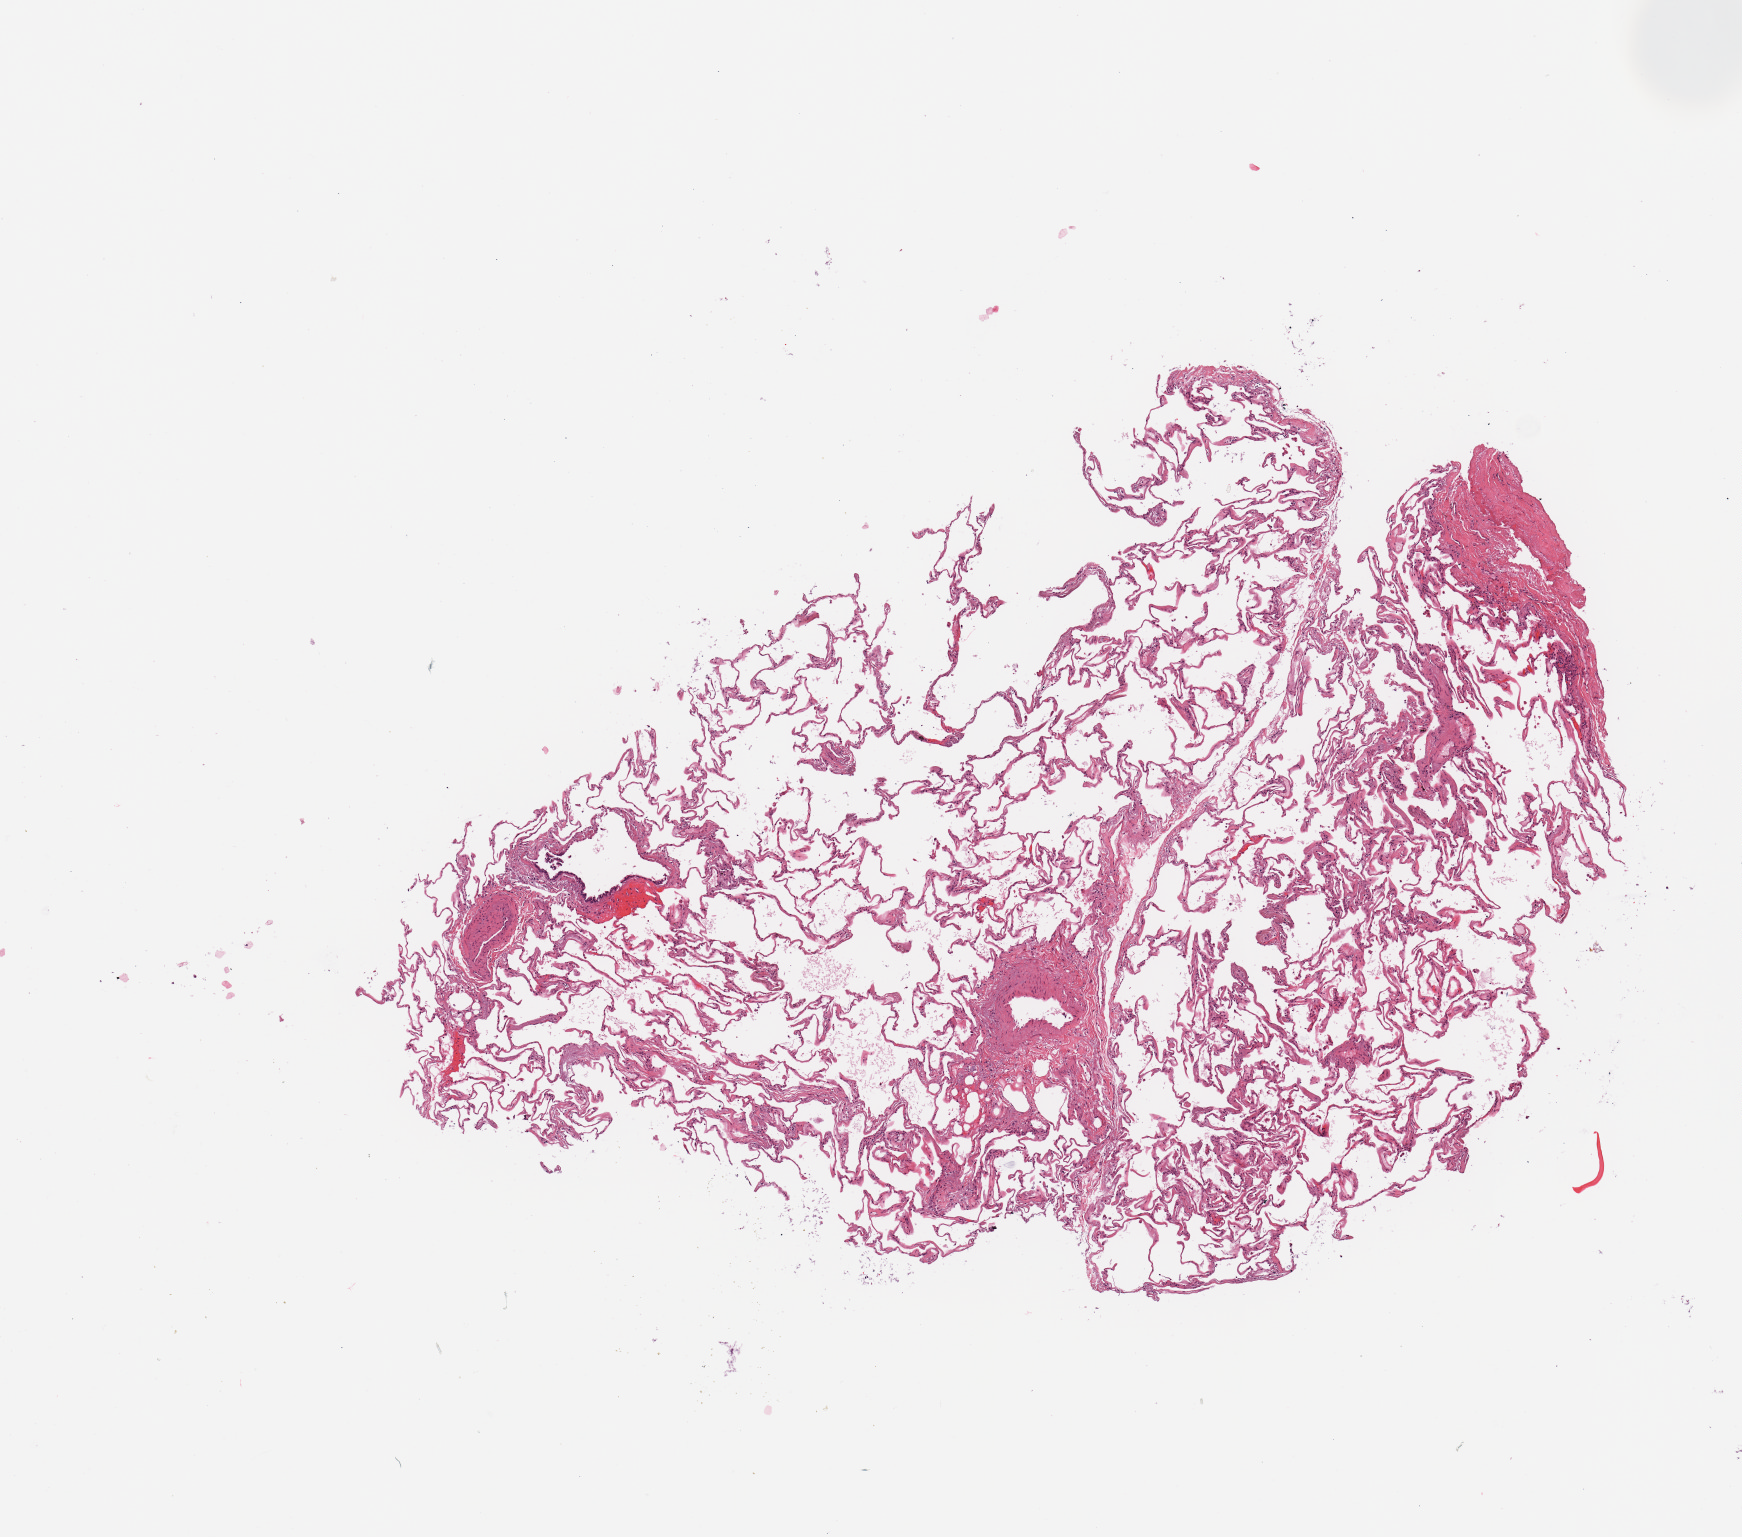
Digitized H&E tissue section (whole slide), low-resolution overview of the scanned area, about 6.9 x 6.1 mm (slide scanned at 20x); normal (non-tumour) tissue sample, sampled site: lung. Patient: female, age 68 years.
This section: normal (non-tumour) tissue from the same patient. Patient diagnosis: Adenocarcinoma, NOS.